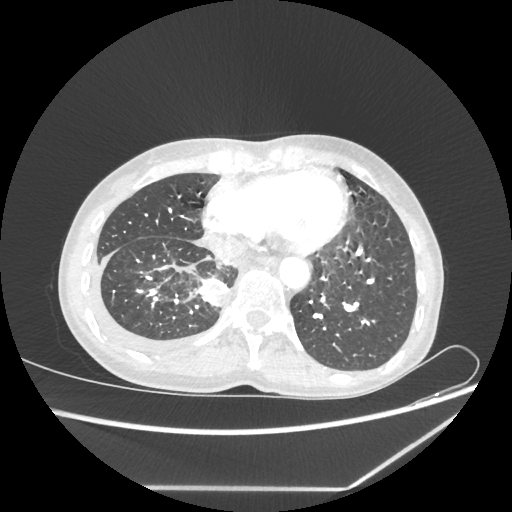
Chest CT, one axial slice; position 67 of 237 along the scan axis; reconstruction kernel STANDARD; lung window (W 1500 / L -600 HU); 1.25 mm slice thickness; 512 × 512 image matrix, field of view 364 × 364 mm. Patient: female, 59 years. From the clinical record (not read from this slice): clinical TNM (as recorded): T1c N1 M1.
Structures marked on this image (bounding box drawn by a radiologist):
- lung tumour (recorded histology: adenocarcinoma): bounding box <198,272,227,311> (left, top, right, bottom; pixels)